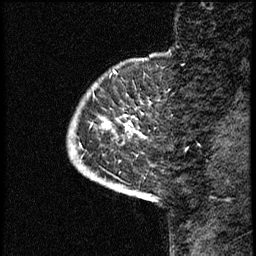
Breast MRI (dynamic contrast-enhanced), one sagittal slice. Position 8 of 68 along the scan axis. Dynamic contrast-enhanced study with each time point stored as its own series, time point 2 of 3 at this slice position (early post-contrast, ordered by acquisition time). 1.5 T. TE 4.2 ms, TR 17.6 ms. 2 mm slice thickness. 256 × 256 image matrix. Female patient, age 52 years. Case-level facts recorded for this patient, not image findings: setting: breast cancer imaged before/during neoadjuvant chemotherapy; receptor status: HER2-positive.
Annotated regions visible in this slice (semi-automatic segmentation, software-assisted and operator-edited):
- analysis volume of interest (the breast-tissue region the enhancement analysis was run in; not a lesion): bounding box (x1, y1, x2, y2) in pixels: (68, 61, 174, 184)
- tumour enhancement mask (voxels above the 100 % enhancement threshold inside the analysis volume of interest): (103, 124, 129, 129)